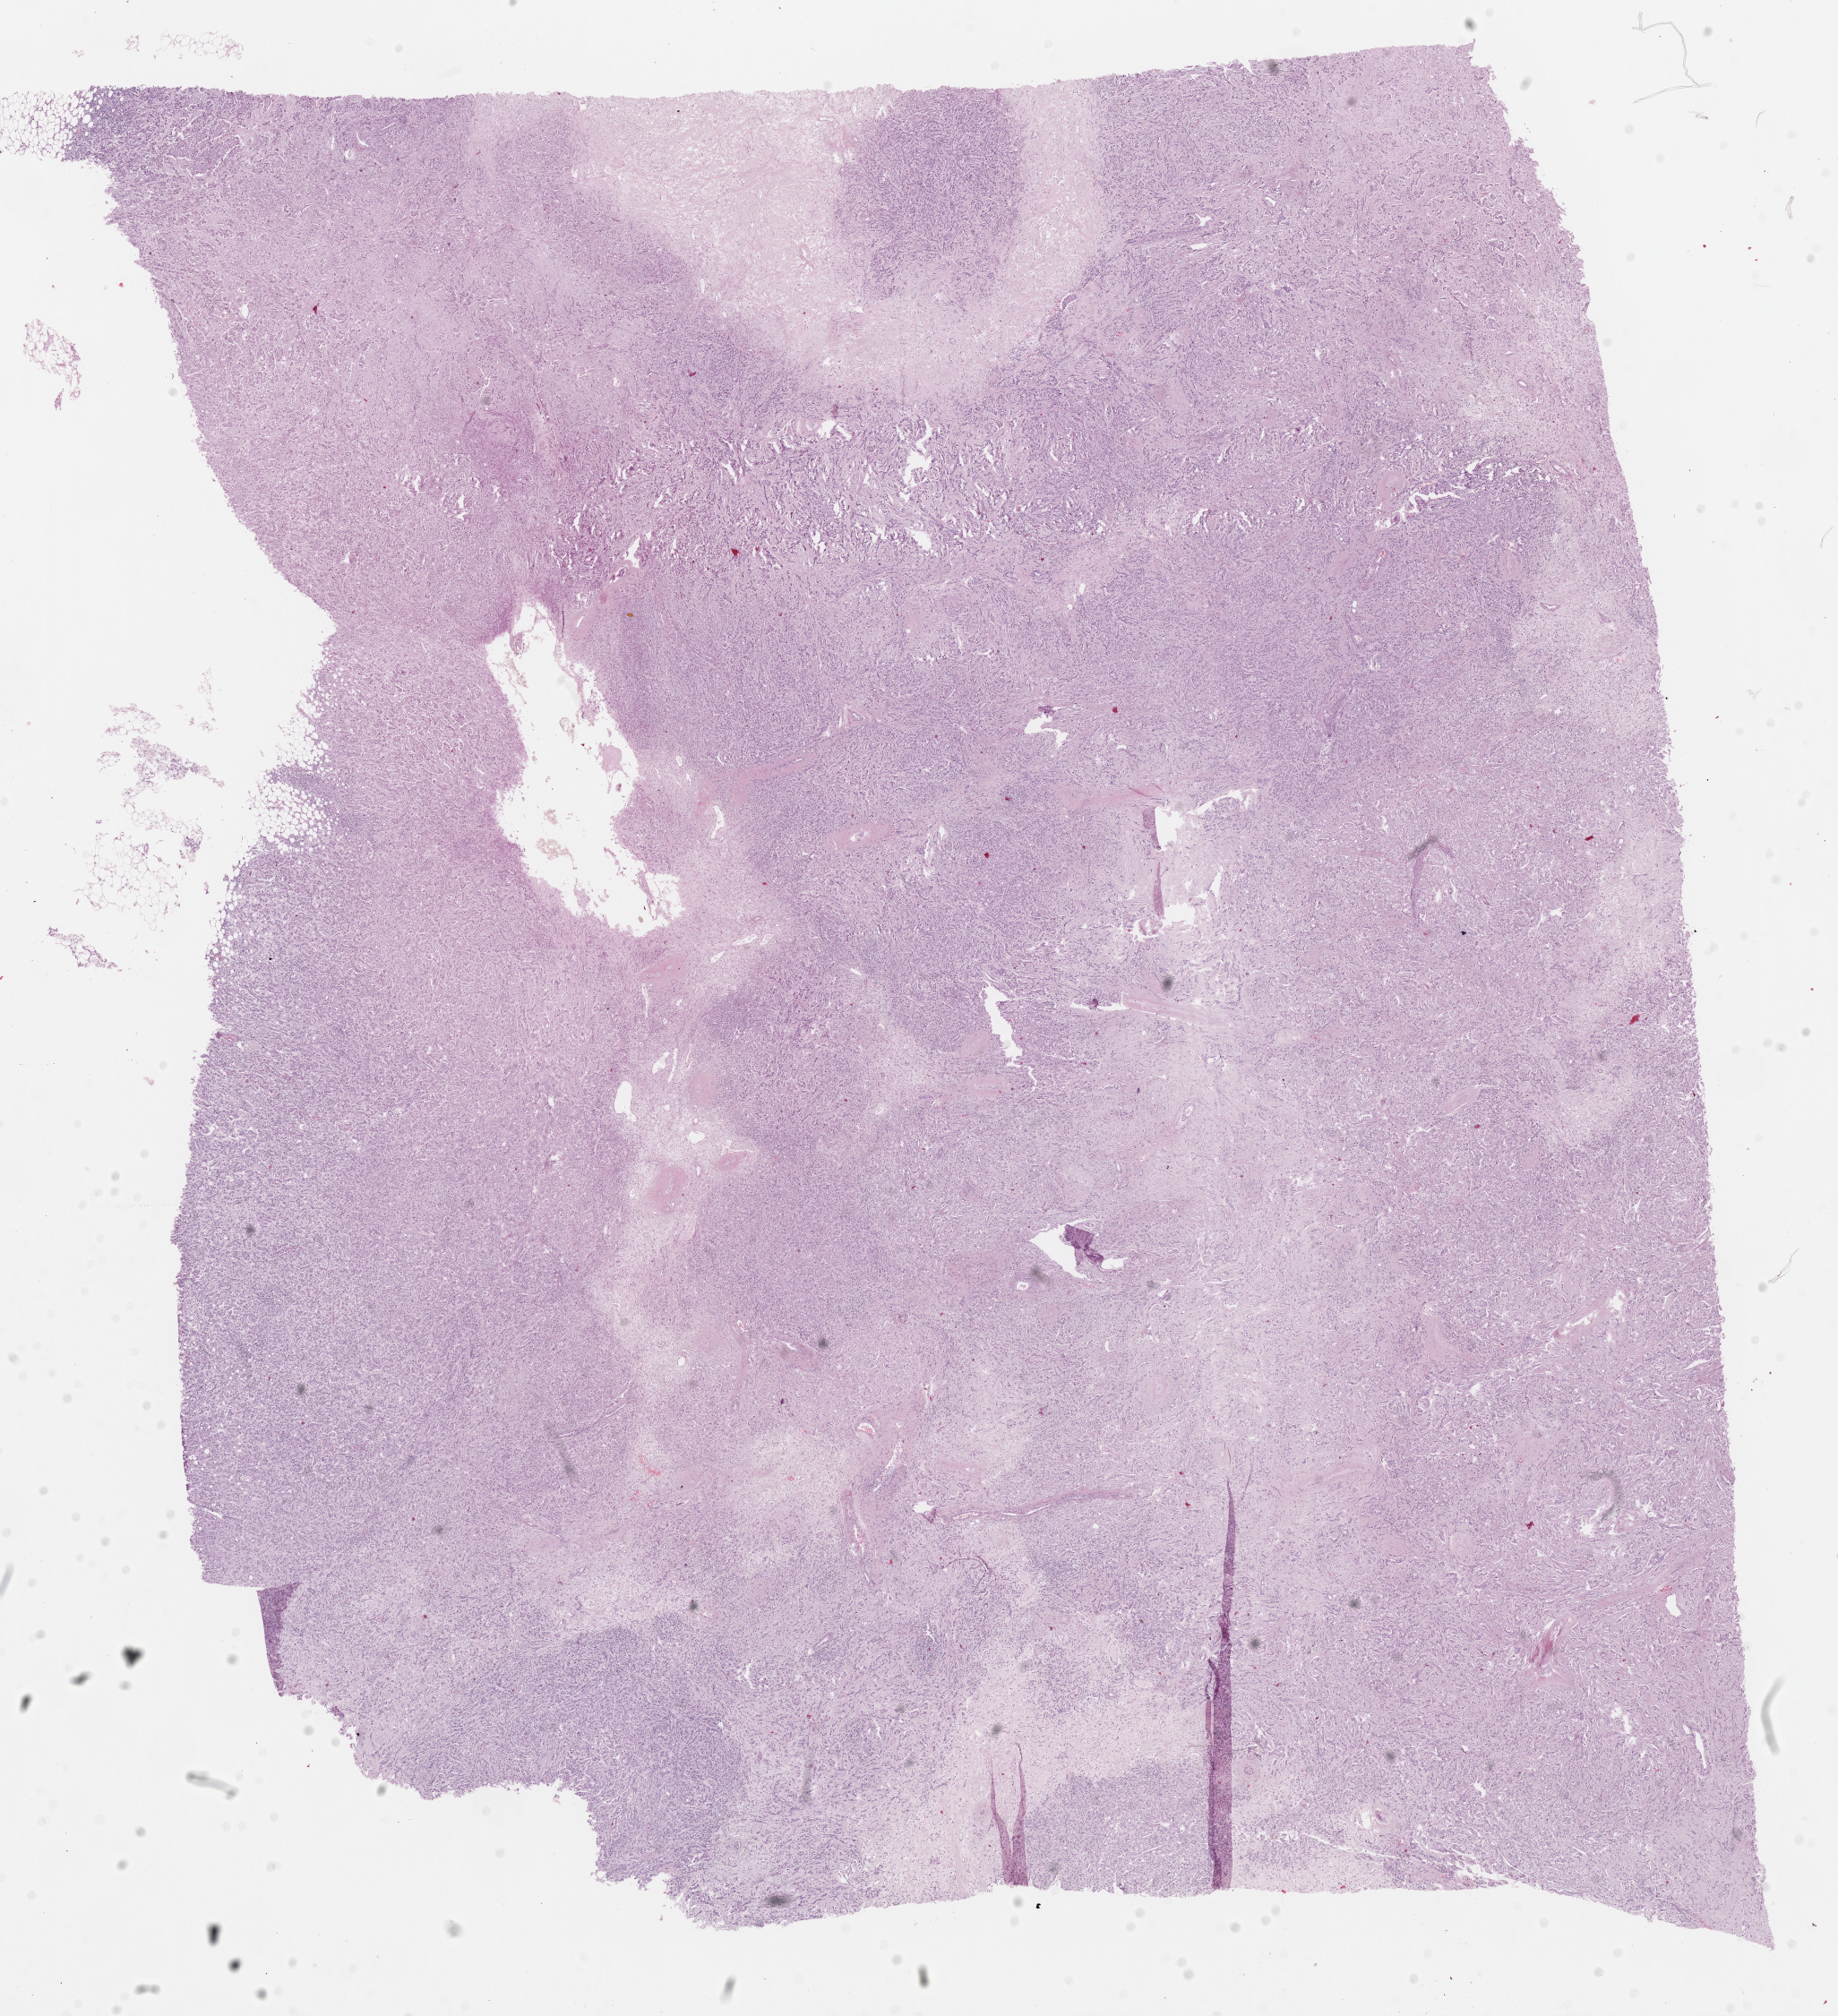
H&E-stained whole-slide image — shown as a low-resolution overview of the whole scanned area (about 16.2 x 17.8 mm), formalin-fixed paraffin-embedded (FFPE) diagnostic section, breast, primary tumour sample. Patient: female, age at initial diagnosis 81 years.
* AJCC pathologic stage: IIIC
* lymph nodes positive (case pathology): 14 of 16 examined
* TNM: T2 N3a MX
* diagnosis: Infiltrating duct carcinoma, NOS